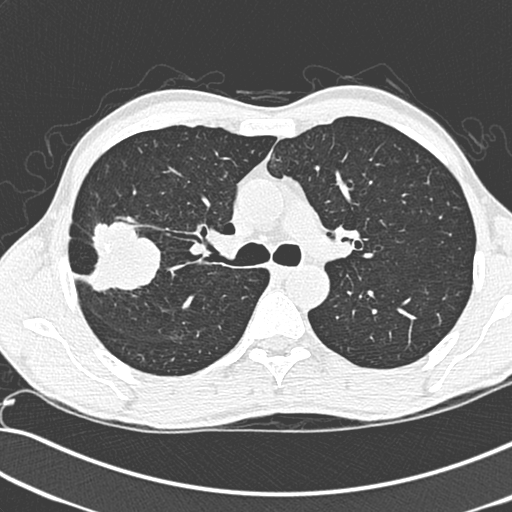
Low-dose screening chest CT, one axial slice. Position 196 of 281 along the scan axis. 120 kVp. Lung window (W 1500 / L -600 HU). 512 × 512 image matrix, field of view 341 × 341 mm.
Outlined on this slice (expert manual segmentation):
- lesion 1 (tumor, upper lobe of right lung): bounding box <78,218,161,294> (left, top, right, bottom; pixels)